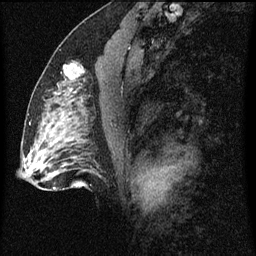
Breast MRI (dynamic contrast-enhanced), one sagittal slice; position 37 of 60 along the scan axis; dynamic contrast-enhanced series, image 2 of 3 at this slice position (ordered by acquisition); 1.5 T; TE 4.2 ms, TR 8 ms; 2 mm slice thickness; 256 × 256 image matrix, field of view 180 × 180 mm. Patient: female, 51 years.
Outlined on this slice (semi-automatically segmented with operator editing):
- analysis volume of interest (the breast-tissue region the enhancement analysis was run in; not a lesion): bounding box [x1, y1, x2, y2] px = [54, 50, 95, 103]
- tumour enhancement mask (voxels above the 70 % enhancement threshold inside the analysis volume of interest): [71, 66, 81, 93]